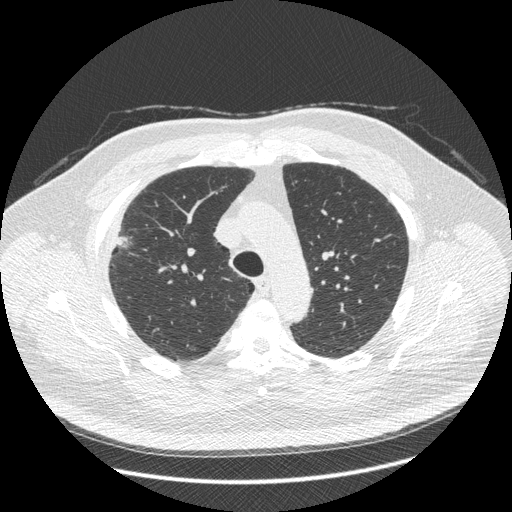
Low-dose screening chest CT, one axial slice. Position 316 of 426 along the scan axis. Lung window (W 1500 / L -600 HU). 1.25 mm slice thickness. 512 × 512 image matrix, field of view 400 × 400 mm.
Structures marked on this image (manually delineated by an expert):
- lesion 1 (tumor, upper lobe of right lung): bounding box (x1, y1, x2, y2) in pixels: (117, 237, 126, 245)